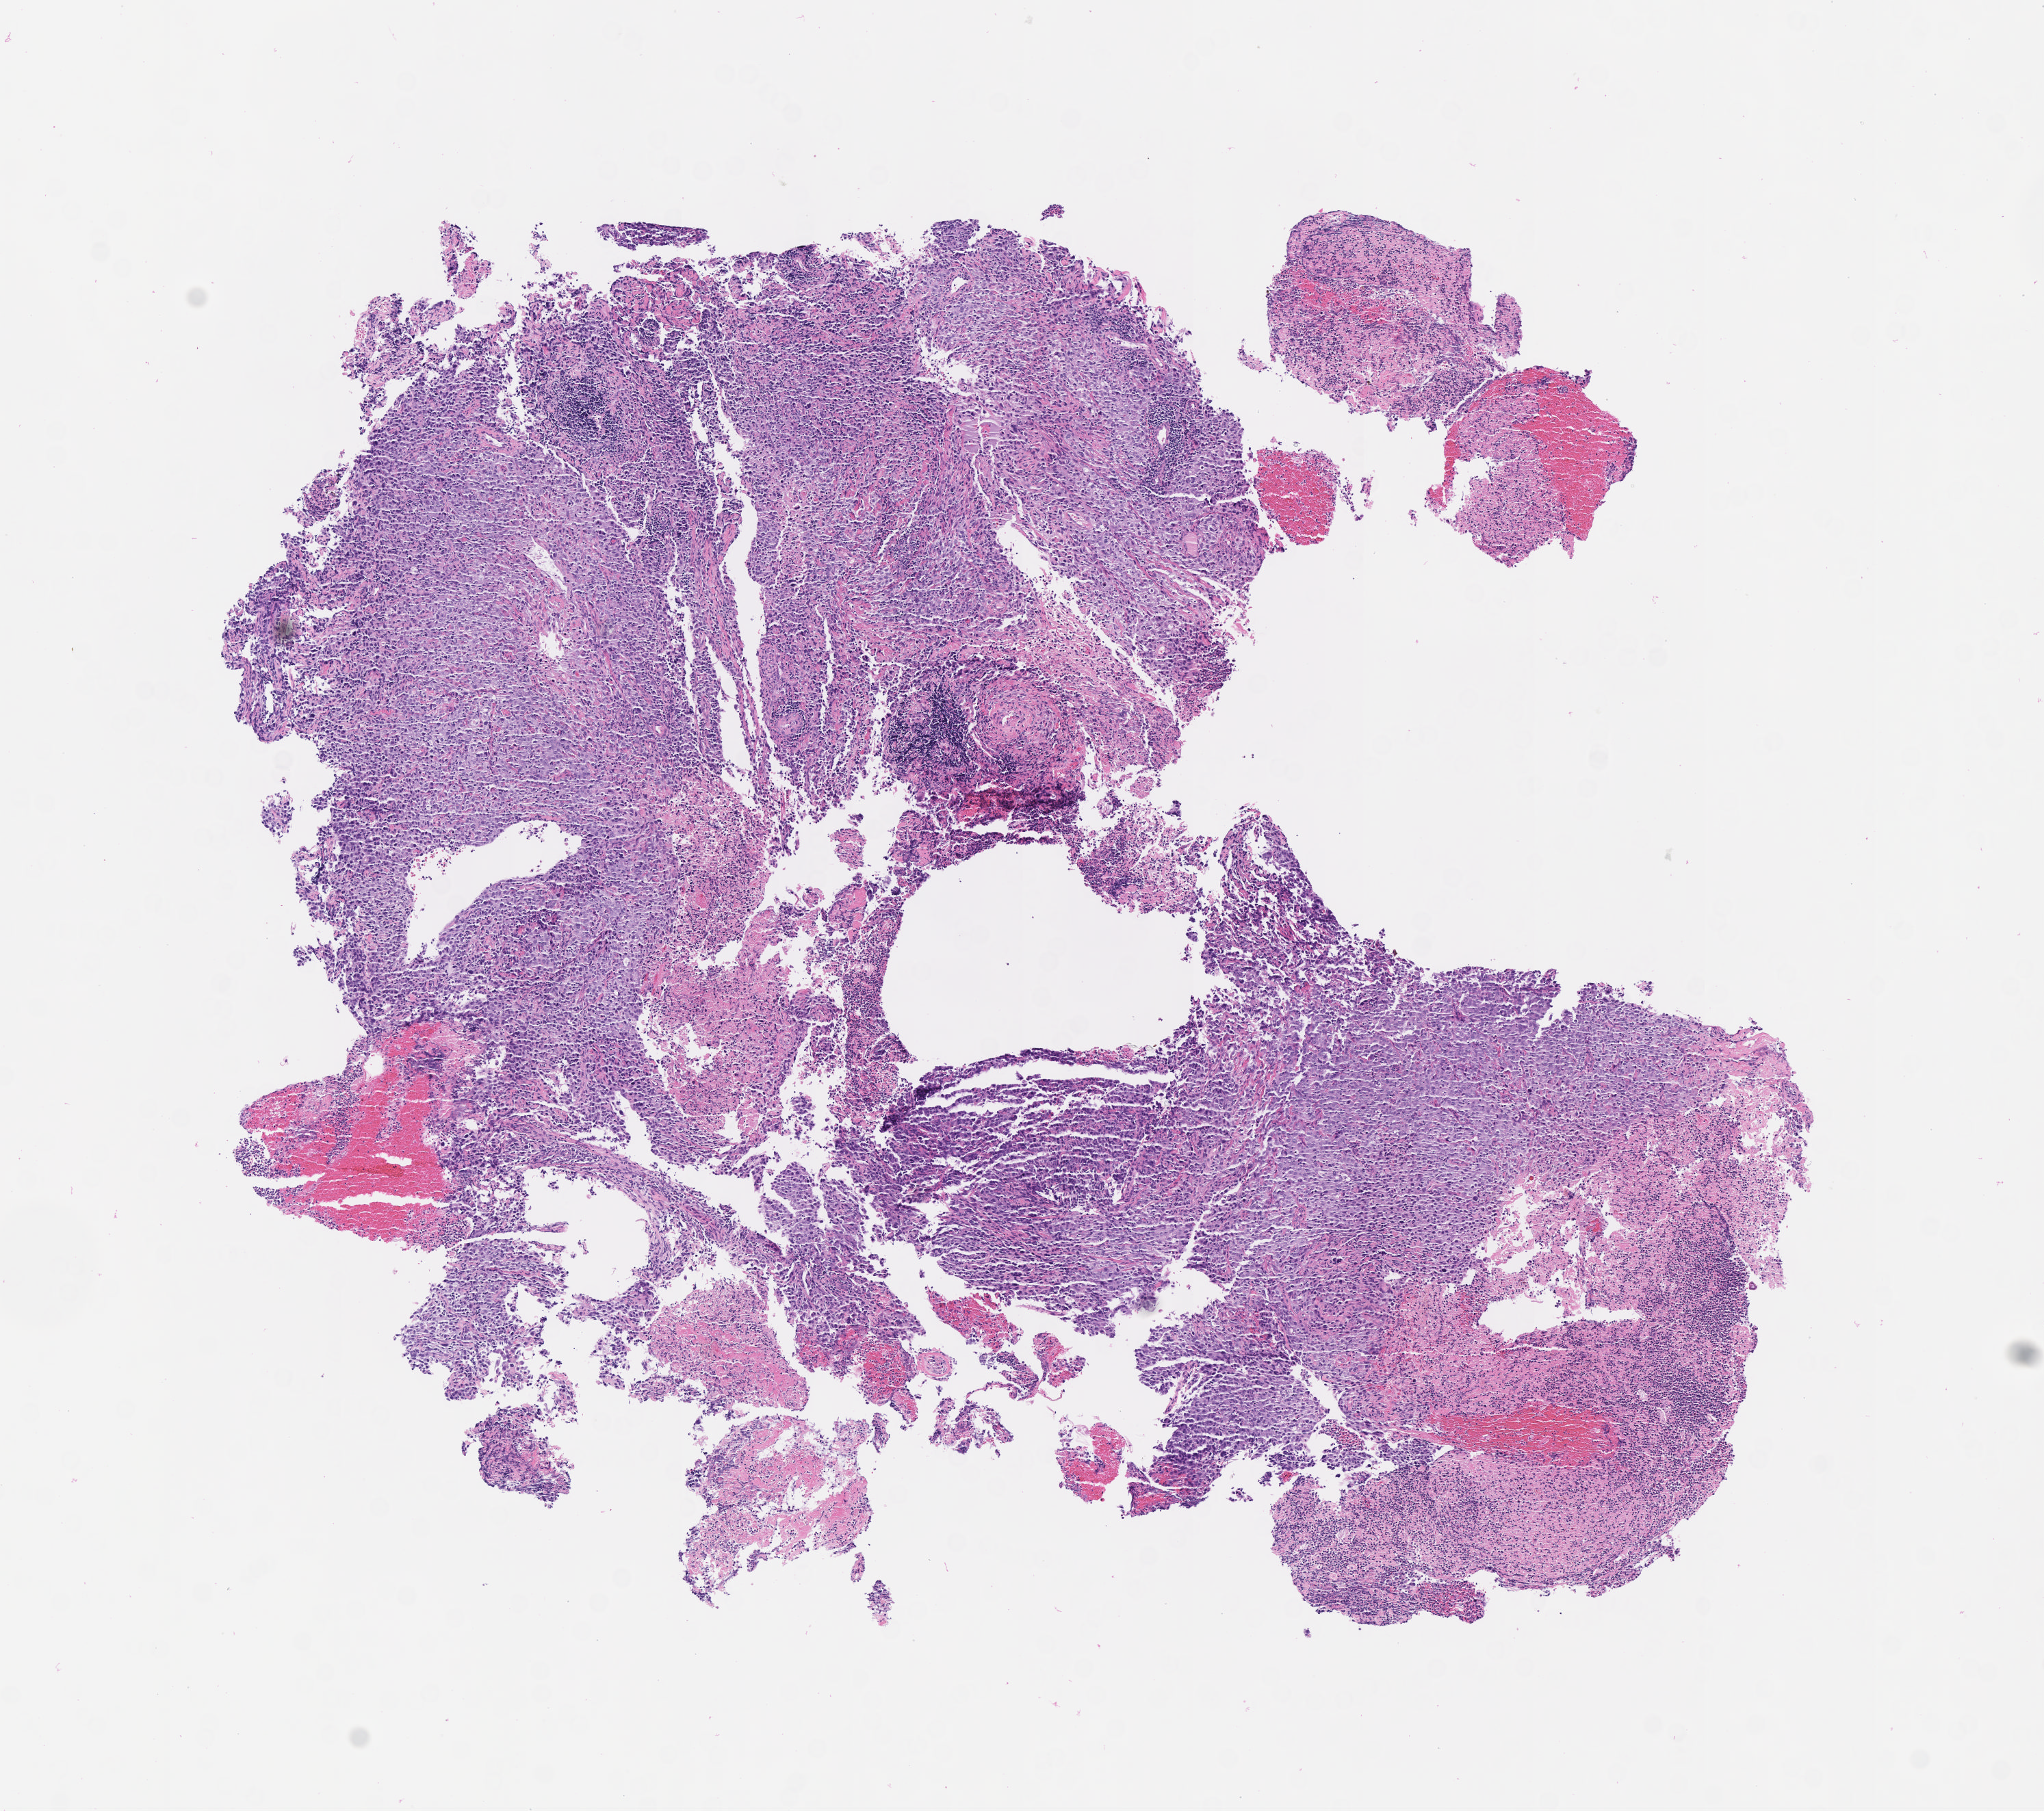
Digitized hematoxylin and eosin (H&E)-stained section — shown as a low-resolution overview of the whole scanned area (about 6.0 x 5.4 mm). Specimen: tumor tissue. Anatomic site: cervix. Patient: female, aged 42.
Histologic diagnosis: Squamous cell carcinoma, large cell, nonkeratinizing, NOS.